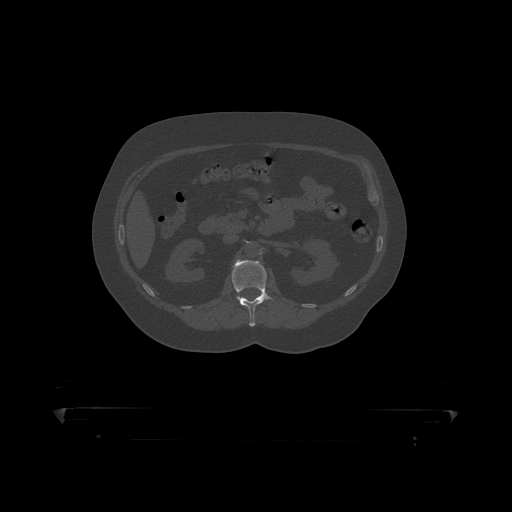
CT including the spine, one axial slice. Position 141 of 390 along the scan axis. Reconstruction kernel STANDARD. 120 kVp. Bone window (W 1800 / L 400 HU). 512 × 512 image matrix, field of view 650 × 650 mm. Male patient, age 60 years. From the clinical record (not read from this slice): primary cancer: prostate.
Structures marked on this image (semi-automatically segmented with operator editing):
- L1 vertebra: bounding box (x1, y1, x2, y2) in pixels: (232, 260, 276, 319)